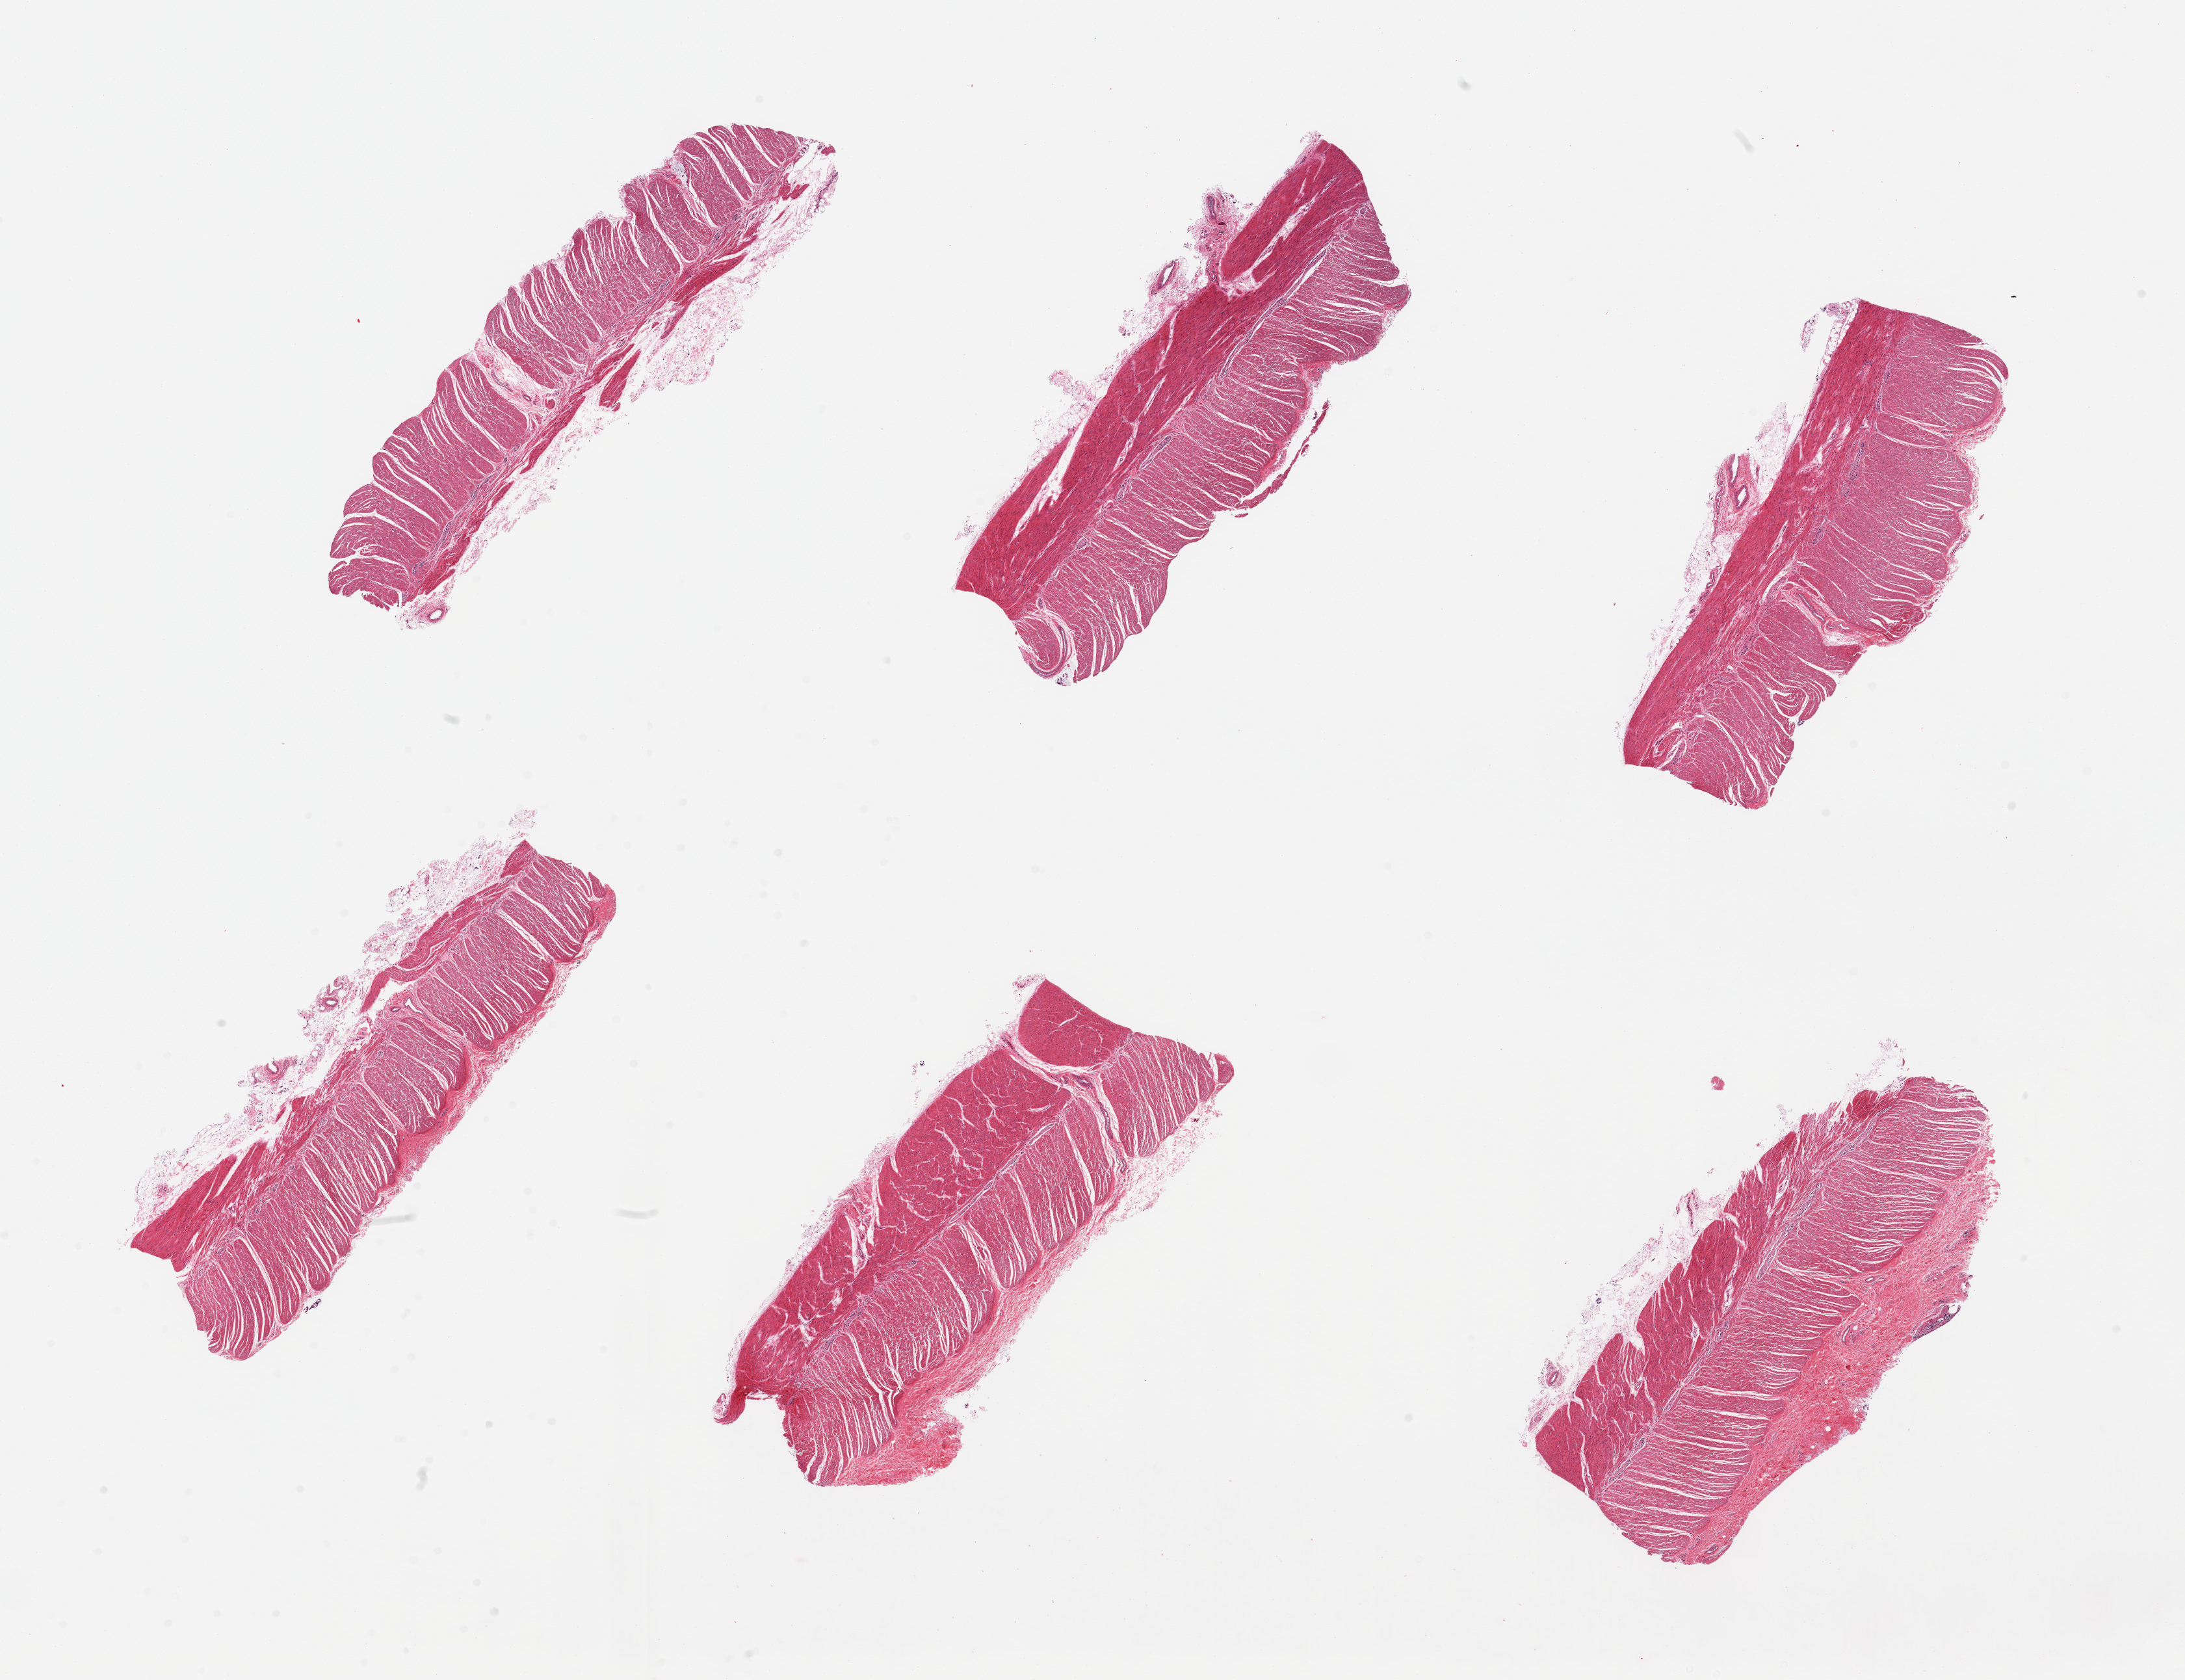
Whole-slide image, hematoxylin and eosin (H&E) stain, brightfield, a low-resolution overview of the entire scanned area, about 26.6 x 20.4 mm (acquisition: 20x scan). PAXgene-fixed, paraffin-embedded tissue. Target tissue: sigmoid colon. Donor tissue sample.
Review note (as recorded): 6 pieces; predominantly well trimmed with small attachment of residual mucosa.